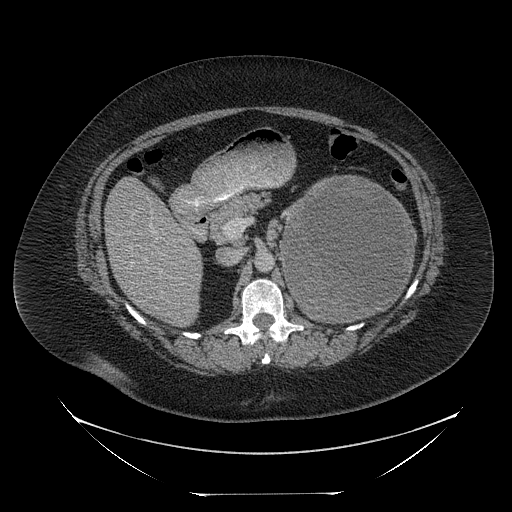
Contrast-enhanced abdominal CT, one axial slice. Slice 137 of 205 in the series (ordered by position). Reconstruction kernel STANDARD. Intravenous contrast given. Soft-tissue window (W 400 / L 40 HU). 2.5 mm slice thickness. 512 × 512 image matrix, field of view 500 × 500 mm. Female patient, age 53 years. Case-level facts recorded for this patient, not image findings: diagnosis: adrenocortical carcinoma; tumour side: left adrenal; tumour size at pathology: 17 cm; Ki-67 index: 20 %; stage (as recorded): 3.
Annotated regions visible in this slice (semi-automatic segmentation, software-assisted and operator-edited):
- mass: bounding box (x1, y1, x2, y2) in pixels: (284, 179, 412, 320)